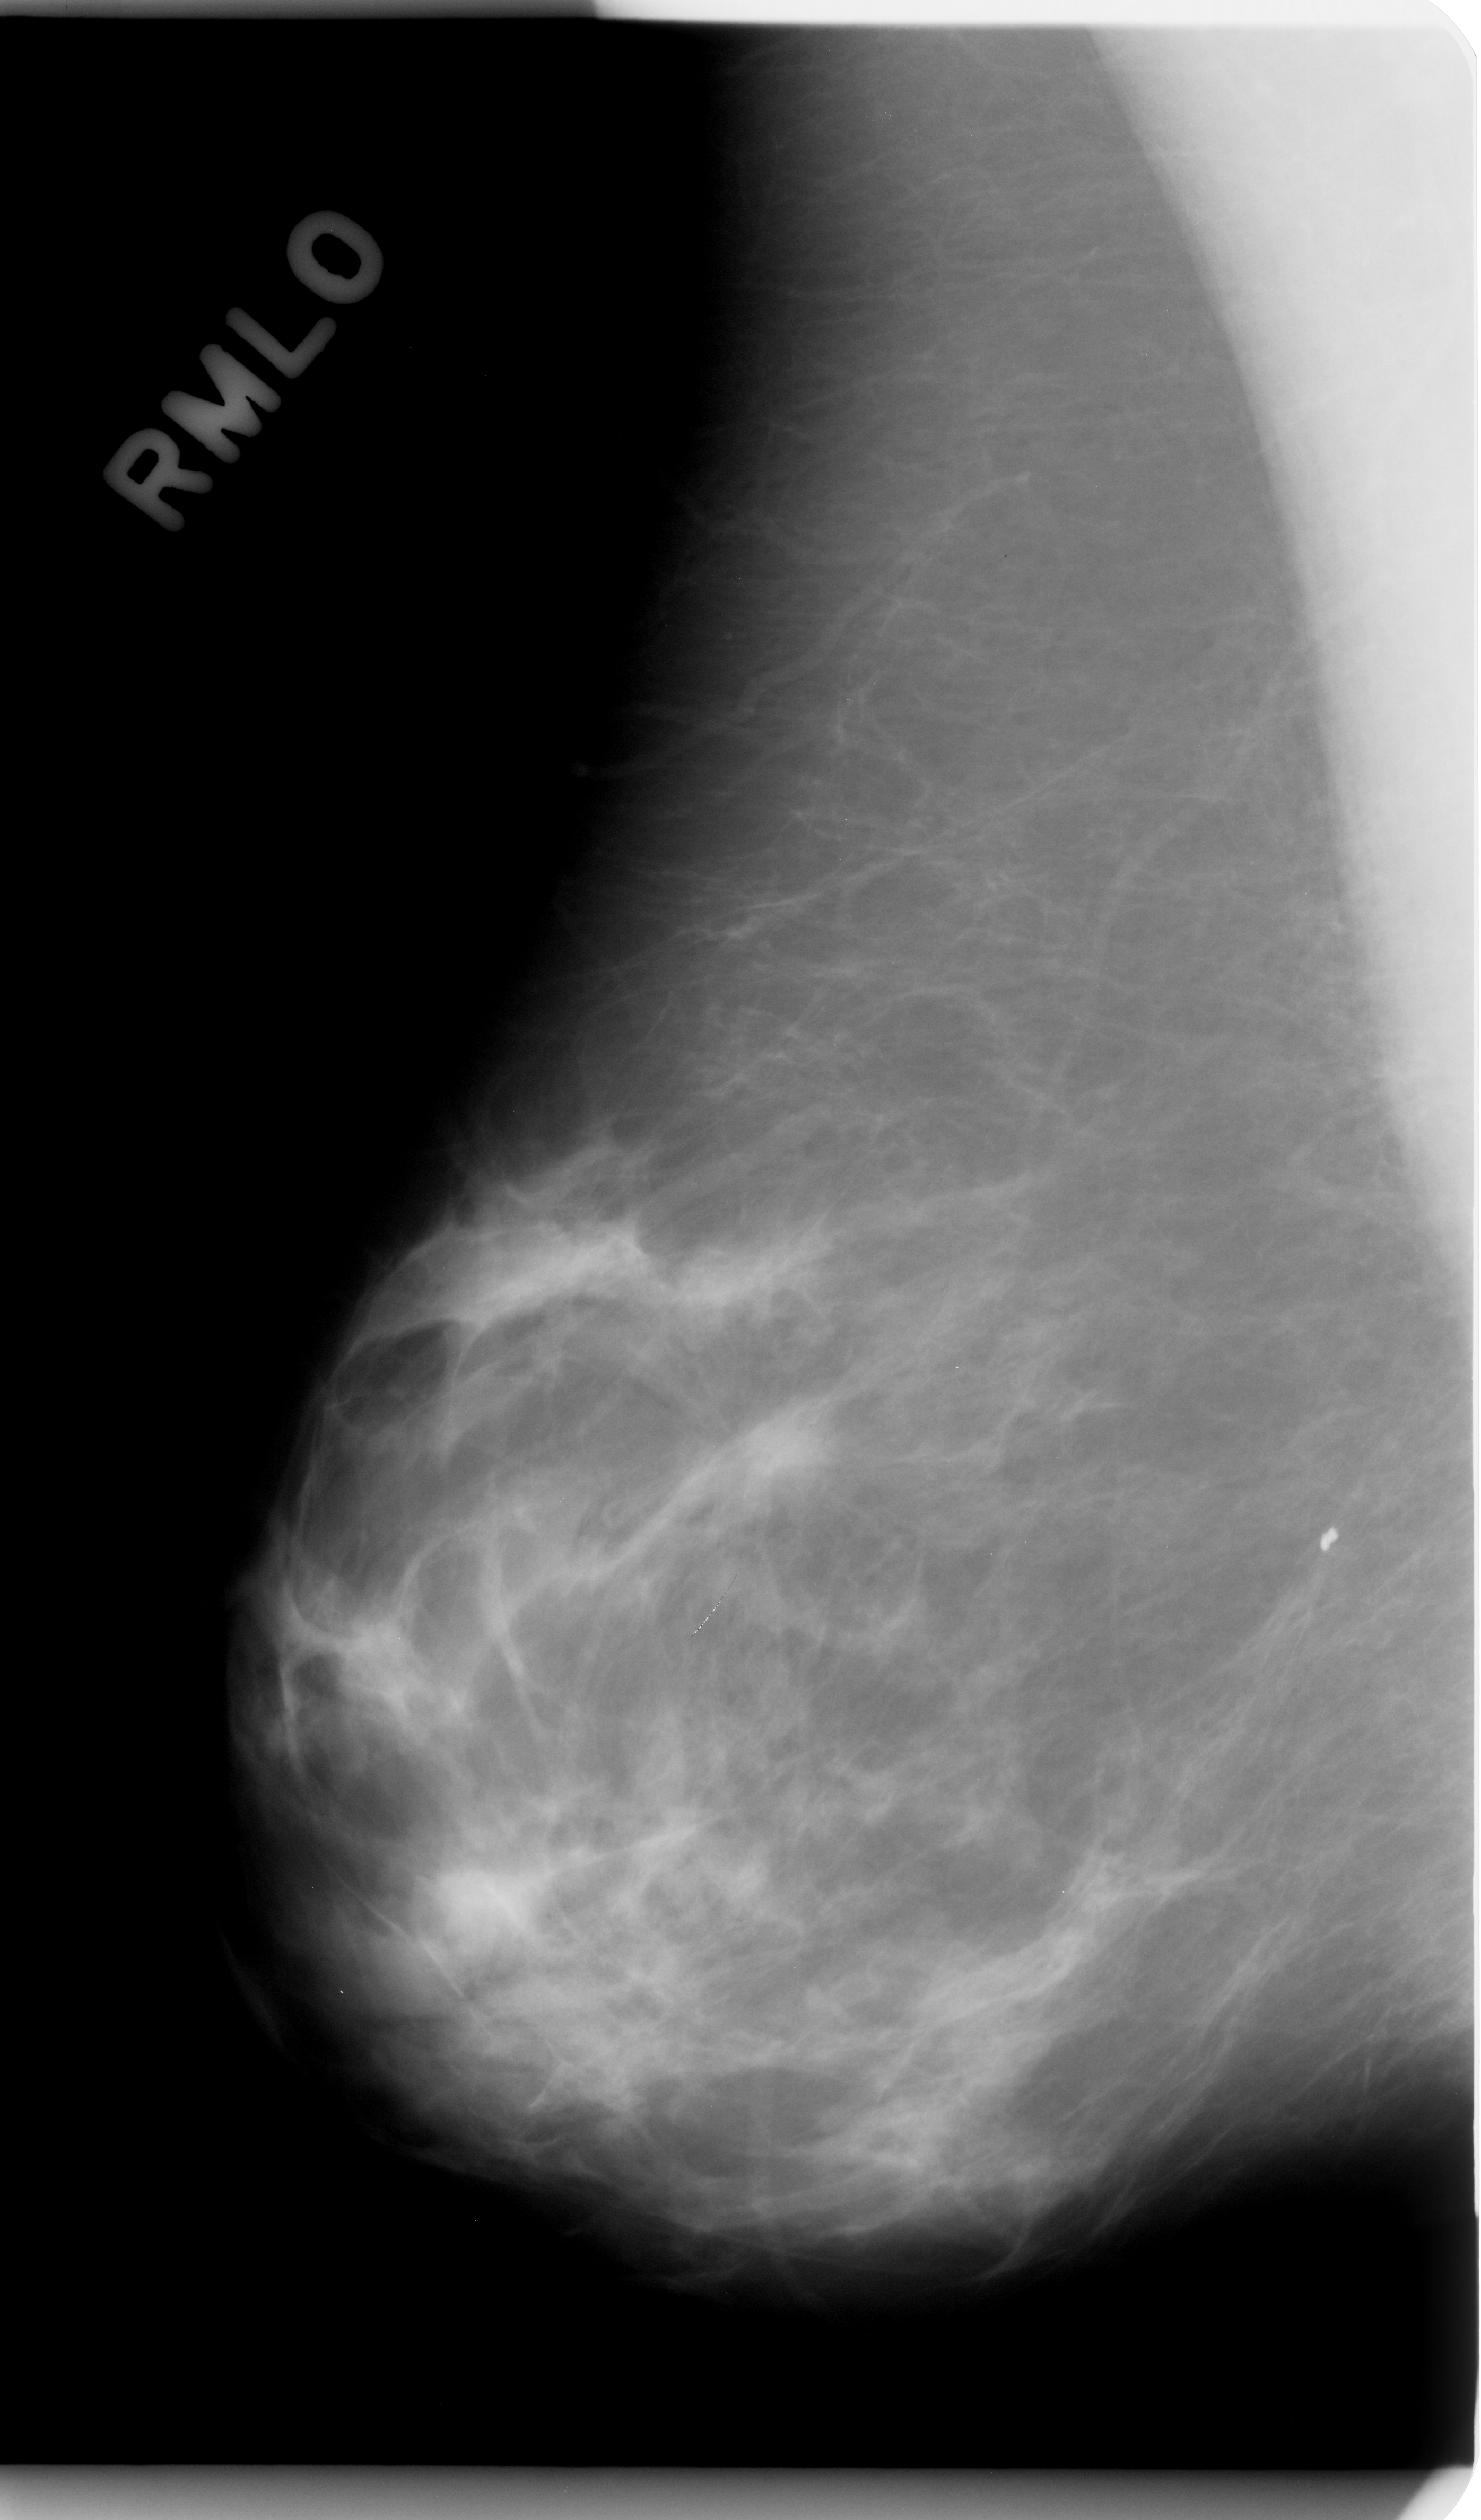
Digitized screen-film mammogram; right breast; MLO view; breast composition: scattered fibroglandular densities (BI-RADS density category 2 of 4); 1481 × 2520 image matrix.
Expert-marked regions of interest on this image (one box per marked abnormality):
- mass, shape irregular, margins spiculated; BI-RADS assessment category 5; subtlety rating 5 on a 1 (subtle) to 5 (obvious) scale; pathology (as recorded): malignant: bounding box [x1, y1, x2, y2] px = [702, 1360, 871, 1524]